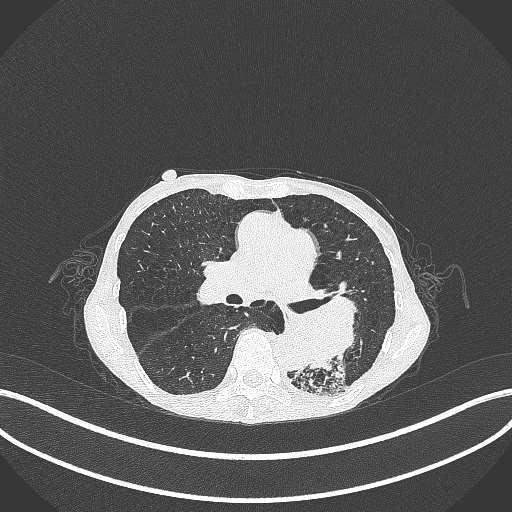
Chest CT, one axial slice. Slice 152 of 347 in the series (ordered by position). Reconstruction kernel B70f. 120 kVp. Lung window (W 1500 / L -600 HU). 512 × 512 image matrix. Female patient, age 70 years. From the clinical record (not read from this slice): clinical TNM (as recorded): T3 N0 M0; histopathological grade: G3.
Outlined on this slice (bounding box drawn by a radiologist):
- lung tumour (recorded histology: small cell carcinoma): bounding box <265,299,369,380> (left, top, right, bottom; pixels)